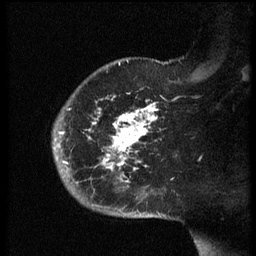
Breast MRI (dynamic contrast-enhanced), one sagittal slice. Dynamic contrast-enhanced series, image 2 of 3 at this slice position (ordered by acquisition). 1.5 T. TE 4.2 ms, TR 8.4 ms. 2.5 mm slice thickness. 256 × 256 image matrix. Patient: female, 38 years. Case-level facts recorded for this patient, not image findings: setting: breast cancer imaged before/during neoadjuvant chemotherapy; receptor status: HER2-positive.
Structures marked on this image (semi-automatically segmented with operator editing):
- analysis volume of interest (the breast-tissue region the enhancement analysis was run in; not a lesion): box from (x=53, y=74) to (x=167, y=202) px
- tumour enhancement mask (voxels above the 70 % enhancement threshold inside the analysis volume of interest): (x=59, y=104)–(x=159, y=183)